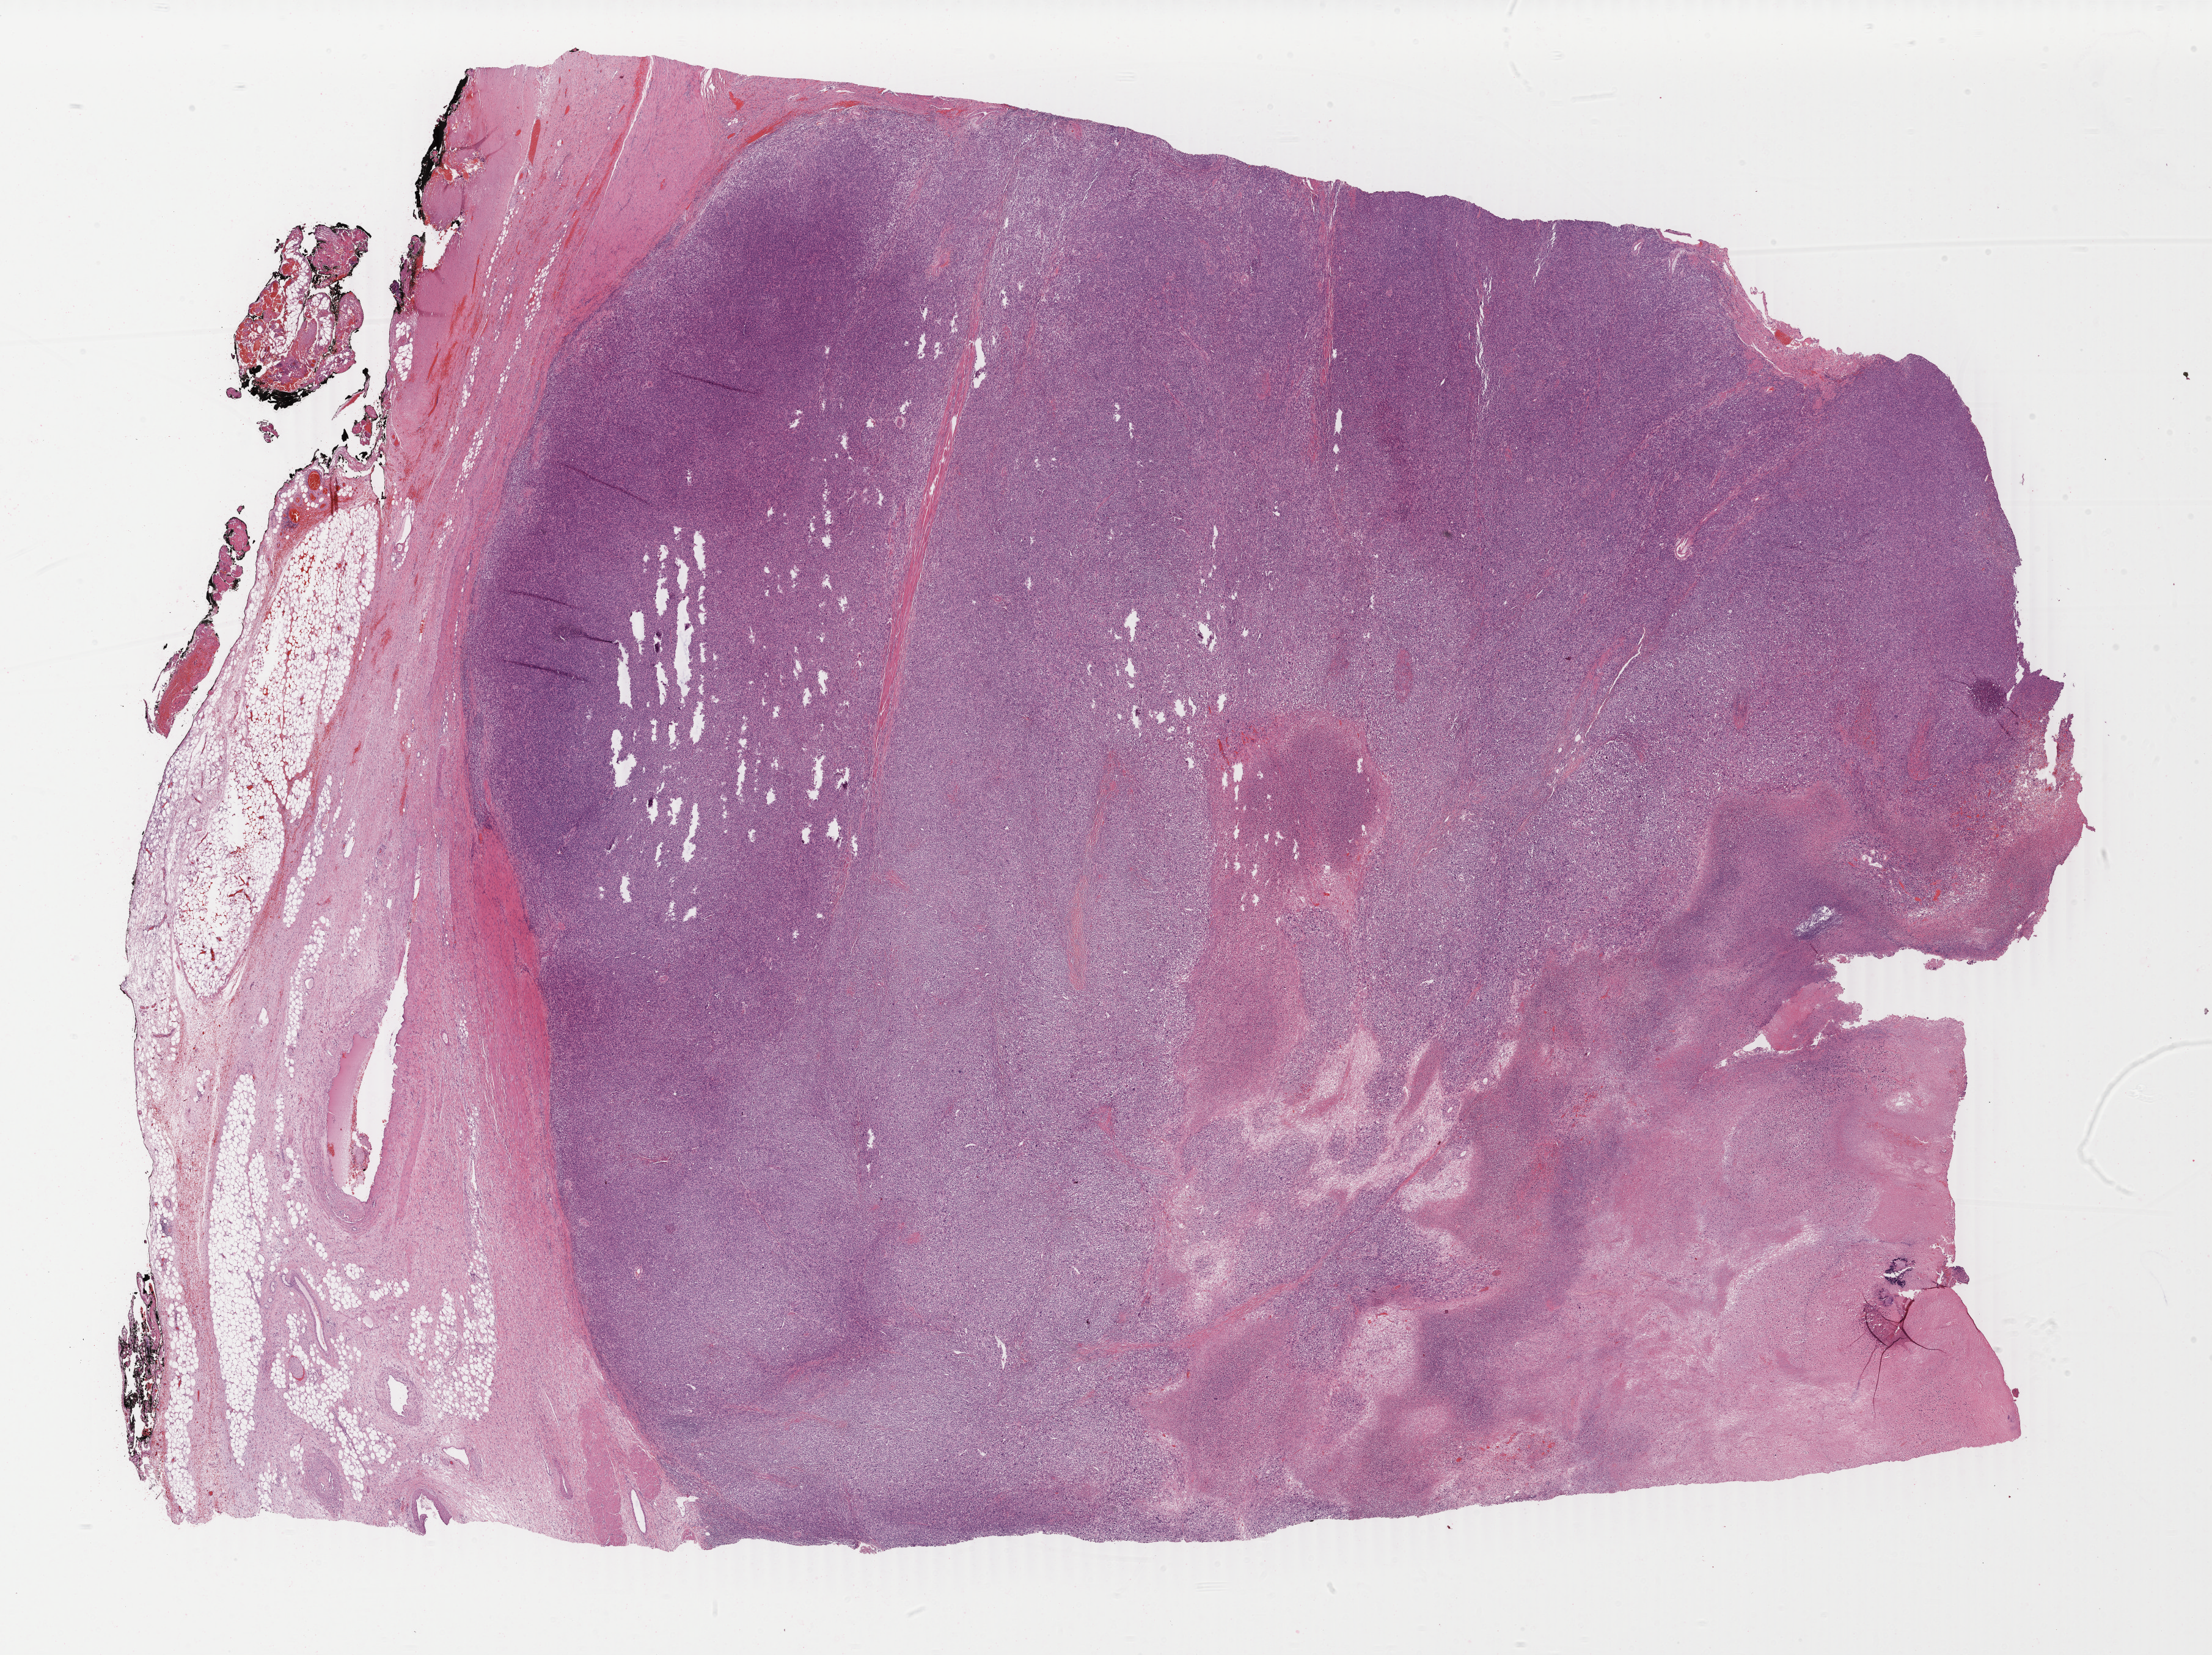
Digitized Hematoxylin and eosin (H&E) stained tissue section (whole slide) — shown as a low-resolution overview of the whole scanned area (about 28.8 x 21.5 mm), formalin-fixed paraffin-embedded (FFPE) diagnostic section, primary tumour sample from the bladder. Patient: male, age at initial diagnosis 69 years.
Pathologic diagnosis: Transitional cell carcinoma (trigone of bladder).